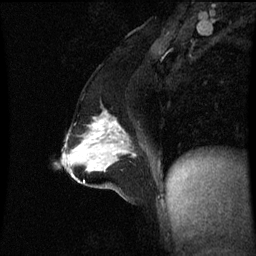
Breast MRI (dynamic contrast-enhanced), one sagittal slice. Slice 32 of 60 in the series (ordered by position). Dynamic contrast-enhanced series, image 2 of 3 at this slice position (ordered by acquisition). 1.5 T. TE 4.2 ms, TR 8.9 ms. 2.1 mm slice thickness. 256 × 256 image matrix, field of view 200 × 200 mm. Female patient, age 47 years. Case-level facts recorded for this patient, not image findings: setting: breast cancer imaged before/during neoadjuvant chemotherapy; receptor status: HR-positive, HER2-negative.
Structures marked on this image (semi-automatically segmented with operator editing):
- analysis volume of interest (the breast-tissue region the enhancement analysis was run in; not a lesion): bounding box <71,116,137,163> (left, top, right, bottom; pixels)
- tumour enhancement mask (voxels above the 70 % enhancement threshold inside the analysis volume of interest): <93,120,136,157>